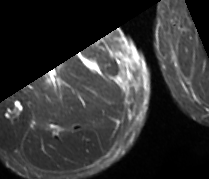
MRI of an extremity soft-tissue mass, one axial slice. Slice 19 of 89 in the series (ordered by position). STIR. MR volume resampled by the dataset authors to the PET/CT grid (not the native acquisition matrix). 3.27 mm slice thickness. 209 × 179 image matrix, field of view 204 × 175 mm. Male patient. From the clinical record (not read from this slice): histological type: undifferentiated - pleiomorphic; grade: high; site of the primary tumour: right thigh.
Annotated regions visible in this slice (expert contour drawn on MRI and transferred to this co-registered scan by the dataset authors):
- gross tumour volume including surrounding oedema: bounding box [x1, y1, x2, y2] px = [48, 69, 61, 83]